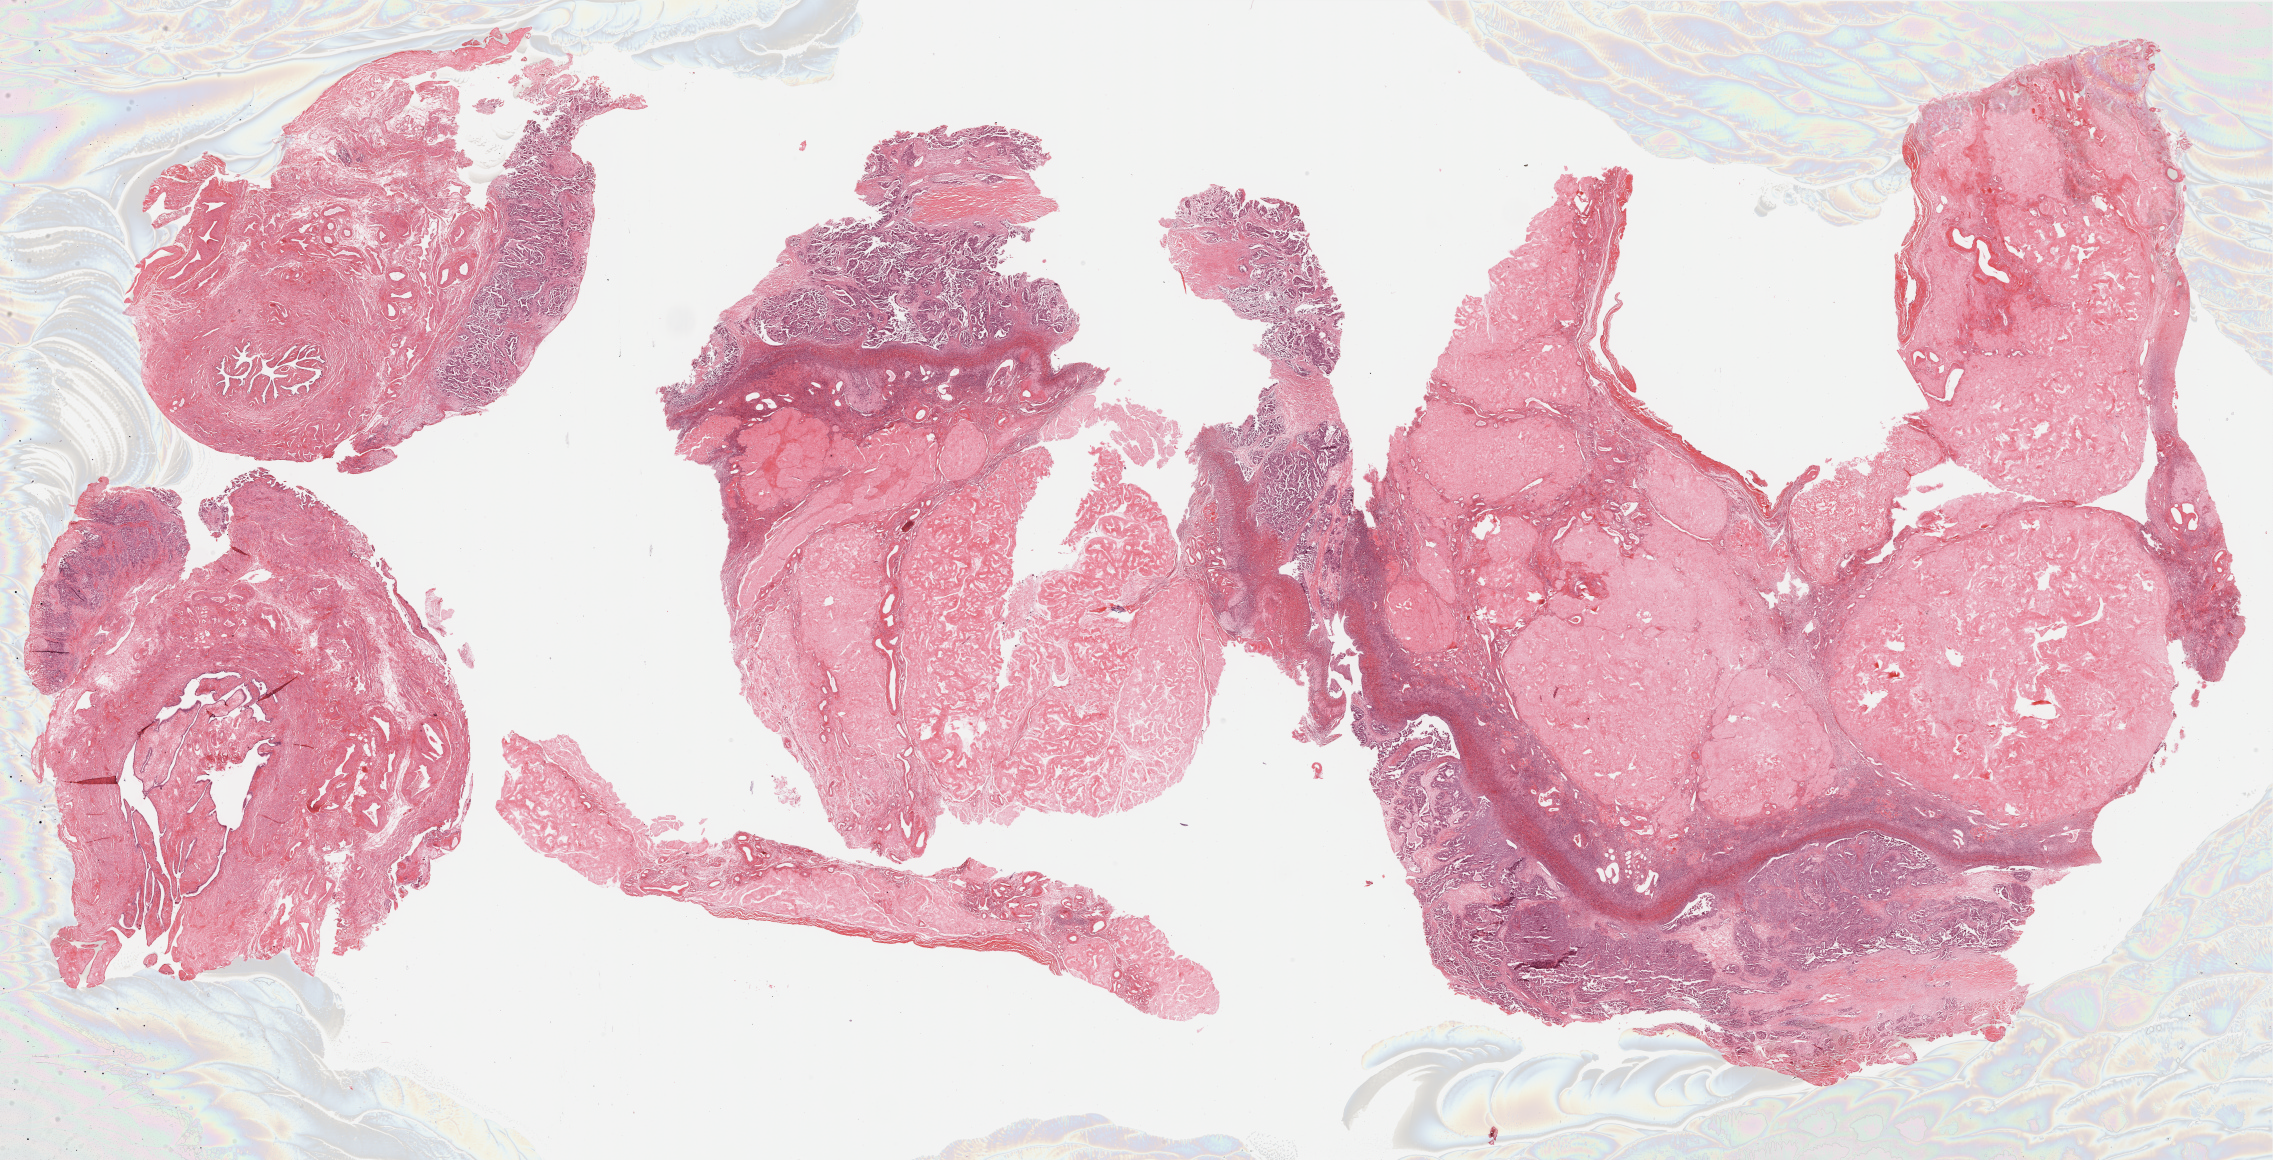
Digitized H&E-stained tissue section (whole slide), whole scanned area (about 36.7 x 18.7 mm) shown as a low-resolution overview, formalin-fixed paraffin-embedded (FFPE) diagnostic section, sample: primary tumour, ovary. Female, age 62 years at initial diagnosis.
Diagnosis: Serous cystadenocarcinoma, NOS.